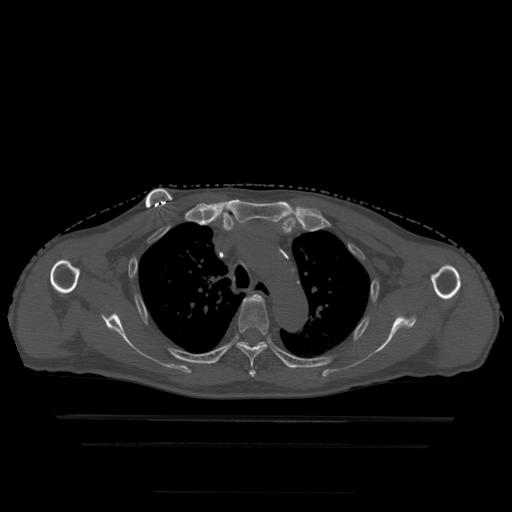
CT including the spine, one axial slice. Slice 352 of 522 in the series (ordered by position). Bone window (W 1800 / L 400 HU). 1.25 mm slice thickness. 512 × 512 image matrix, field of view 436 × 436 mm. Patient age 68 years. From the clinical record (not read from this slice): primary cancer: urothelial.
Annotated regions visible in this slice (semi-automatic segmentation, software-assisted and operator-edited):
- T3 vertebra: bounding box [x1, y1, x2, y2] px = [255, 295, 262, 300]
- T4 vertebra: [236, 295, 269, 378]
- T5 vertebra: [241, 342, 265, 347]